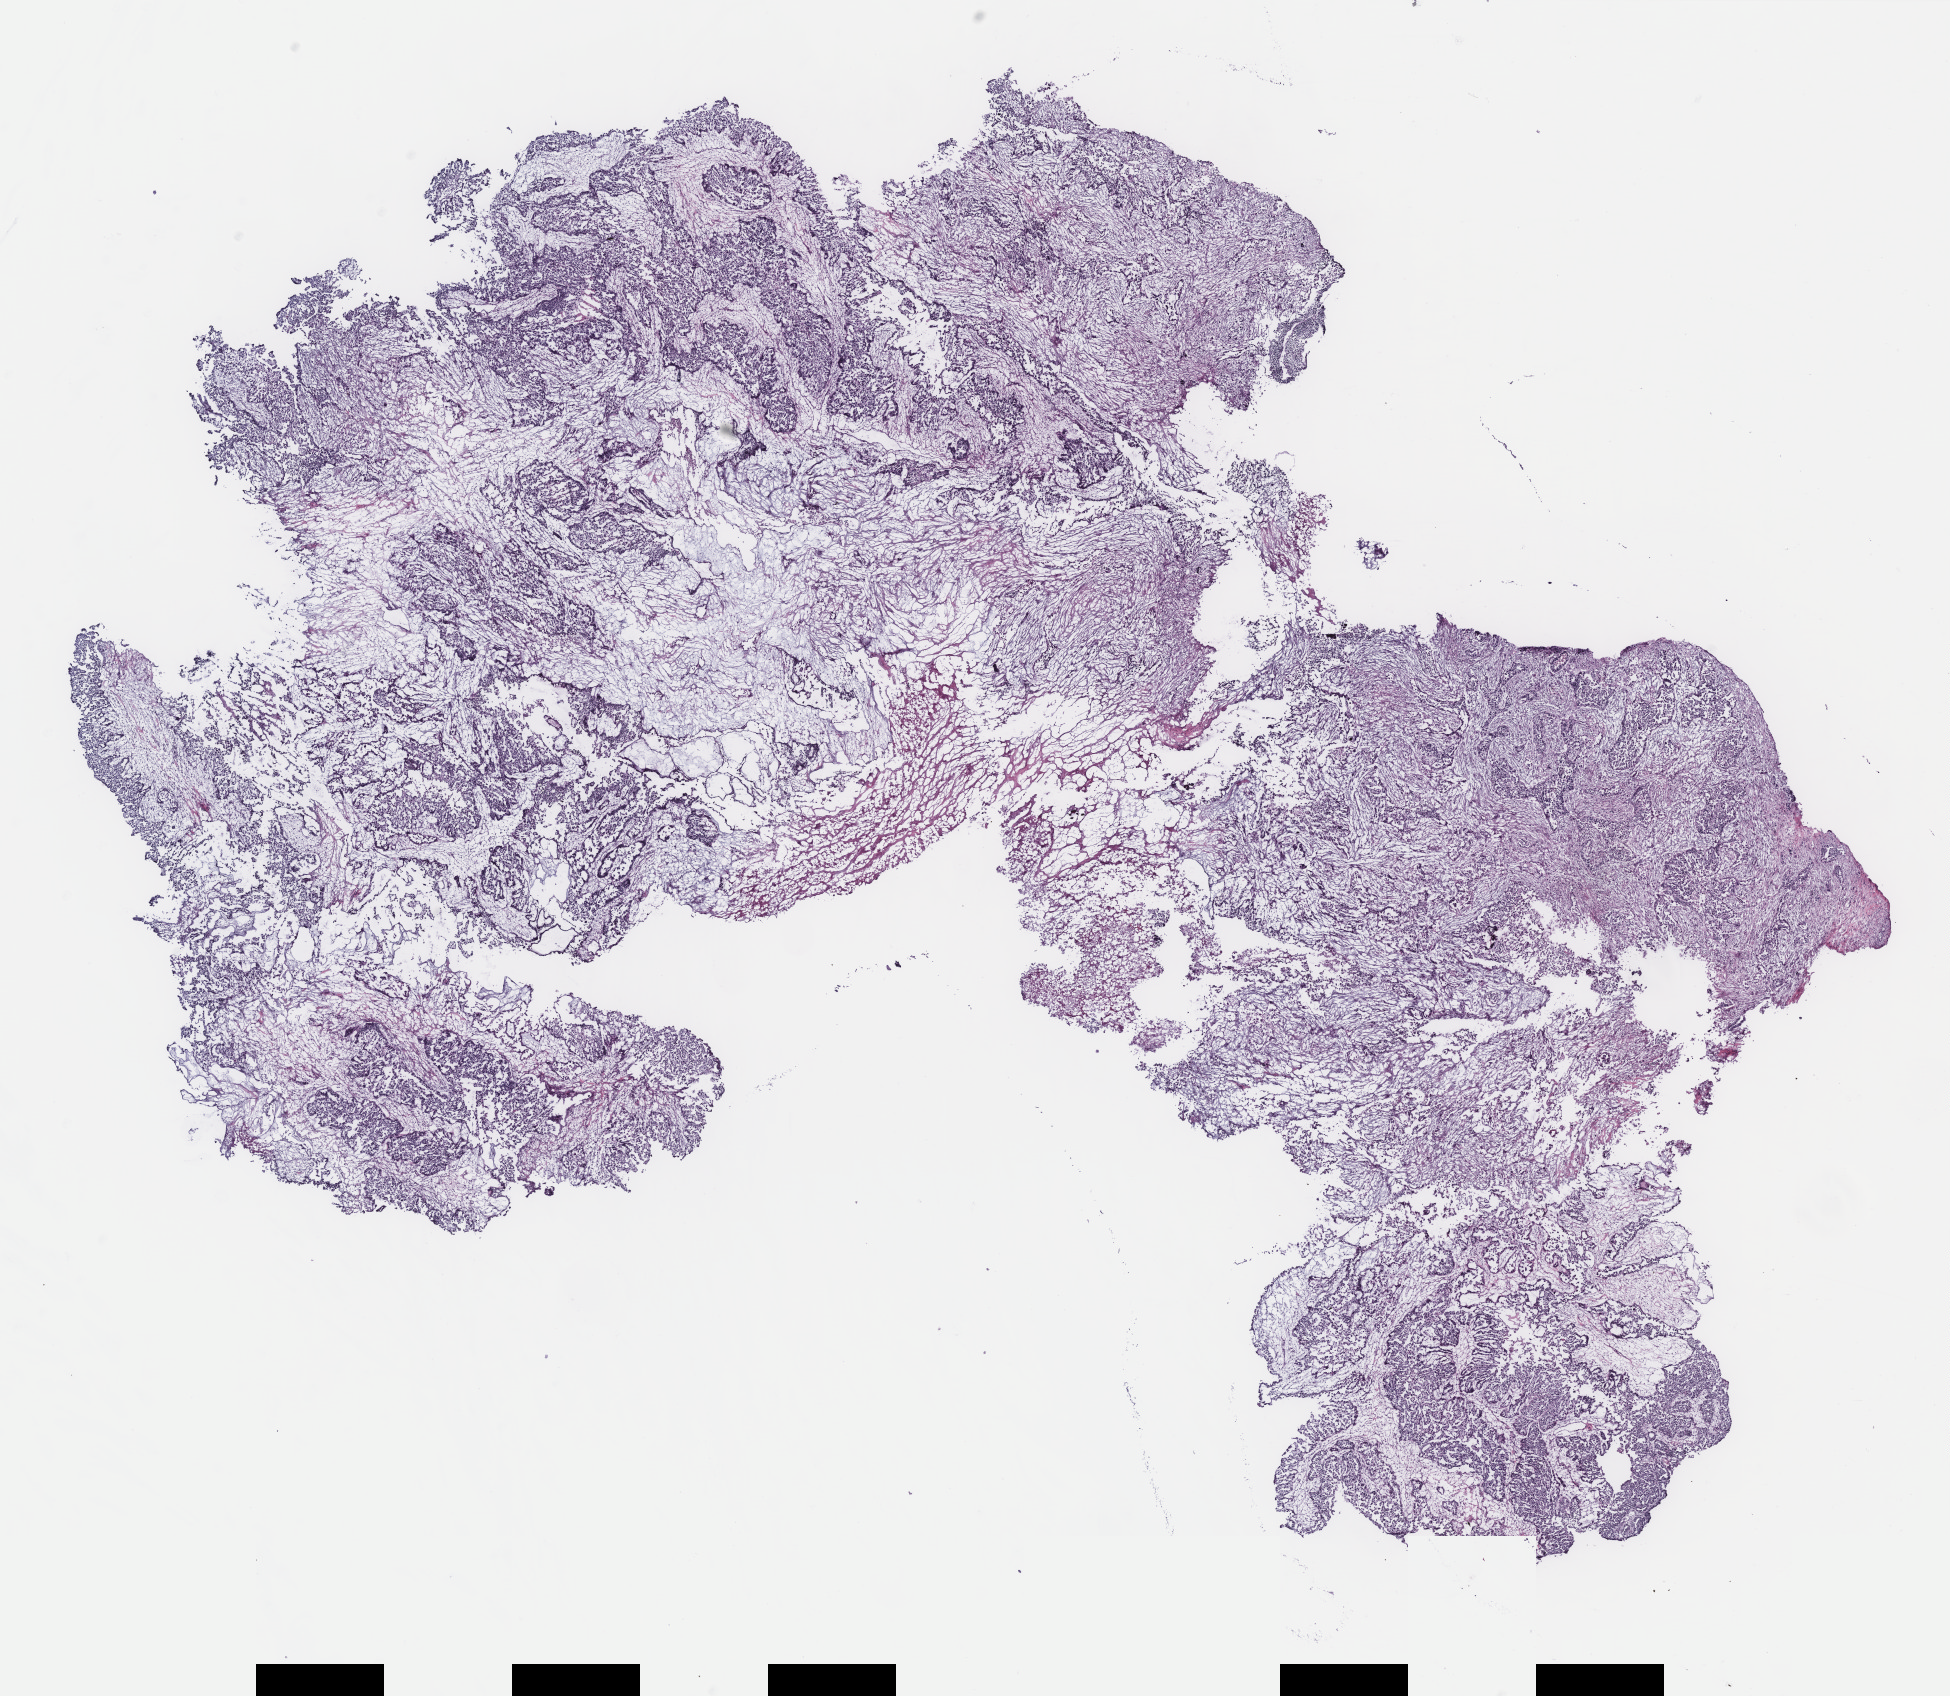
Hematoxylin and eosin (H&E) stained whole-slide image — low-resolution overview of the scanned area, about 15.6 x 13.6 mm (slide scanned at 40x). Ovary, tumour tissue. Female, 68 y/o.
Diagnosis: Serous adenocarcinoma, NOS. Primary tumour site (as recorded): ovary.